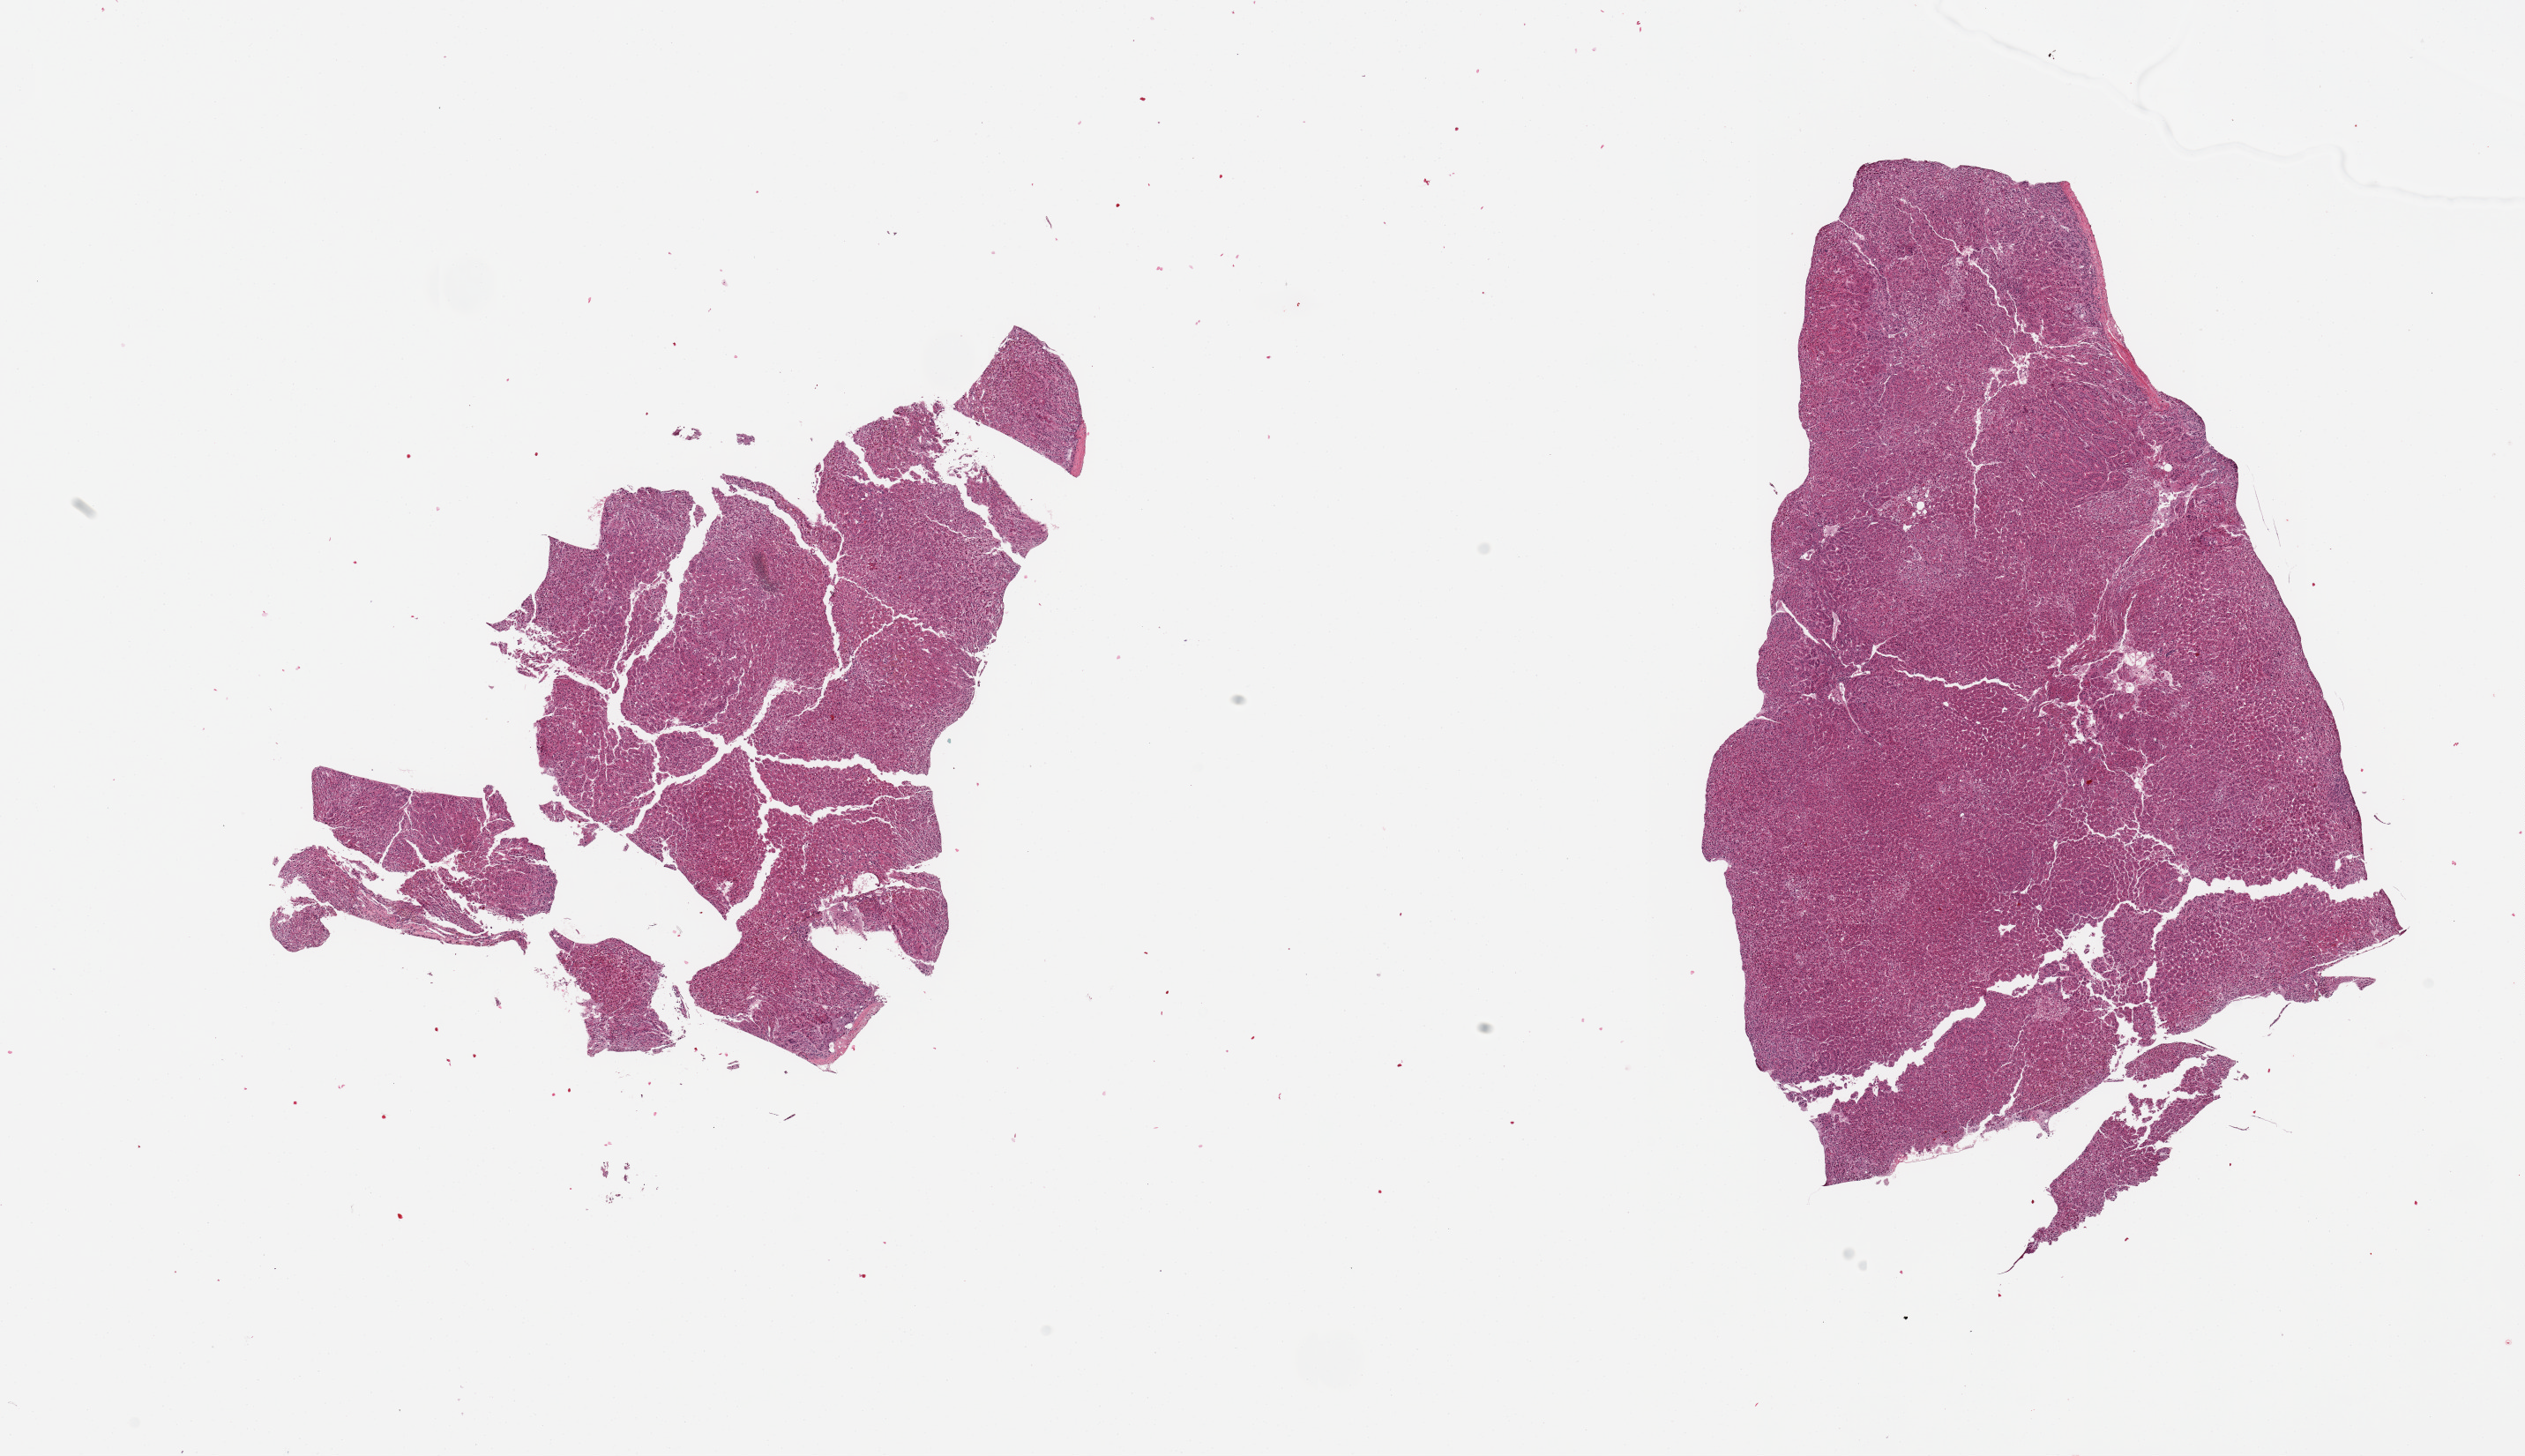
Haematoxylin and eosin whole-slide image, a low-resolution overview of the entire scanned area, about 22.6 x 13.1 mm (from a 20x scan). PAXgene-fixed paraffin-embedded (PFPE) section. Section of adrenal gland (target tissue). Donor tissue sample. Donor sex: female.
* reviewer comment on this tissue sample: 2 pieces, well preserved cortex